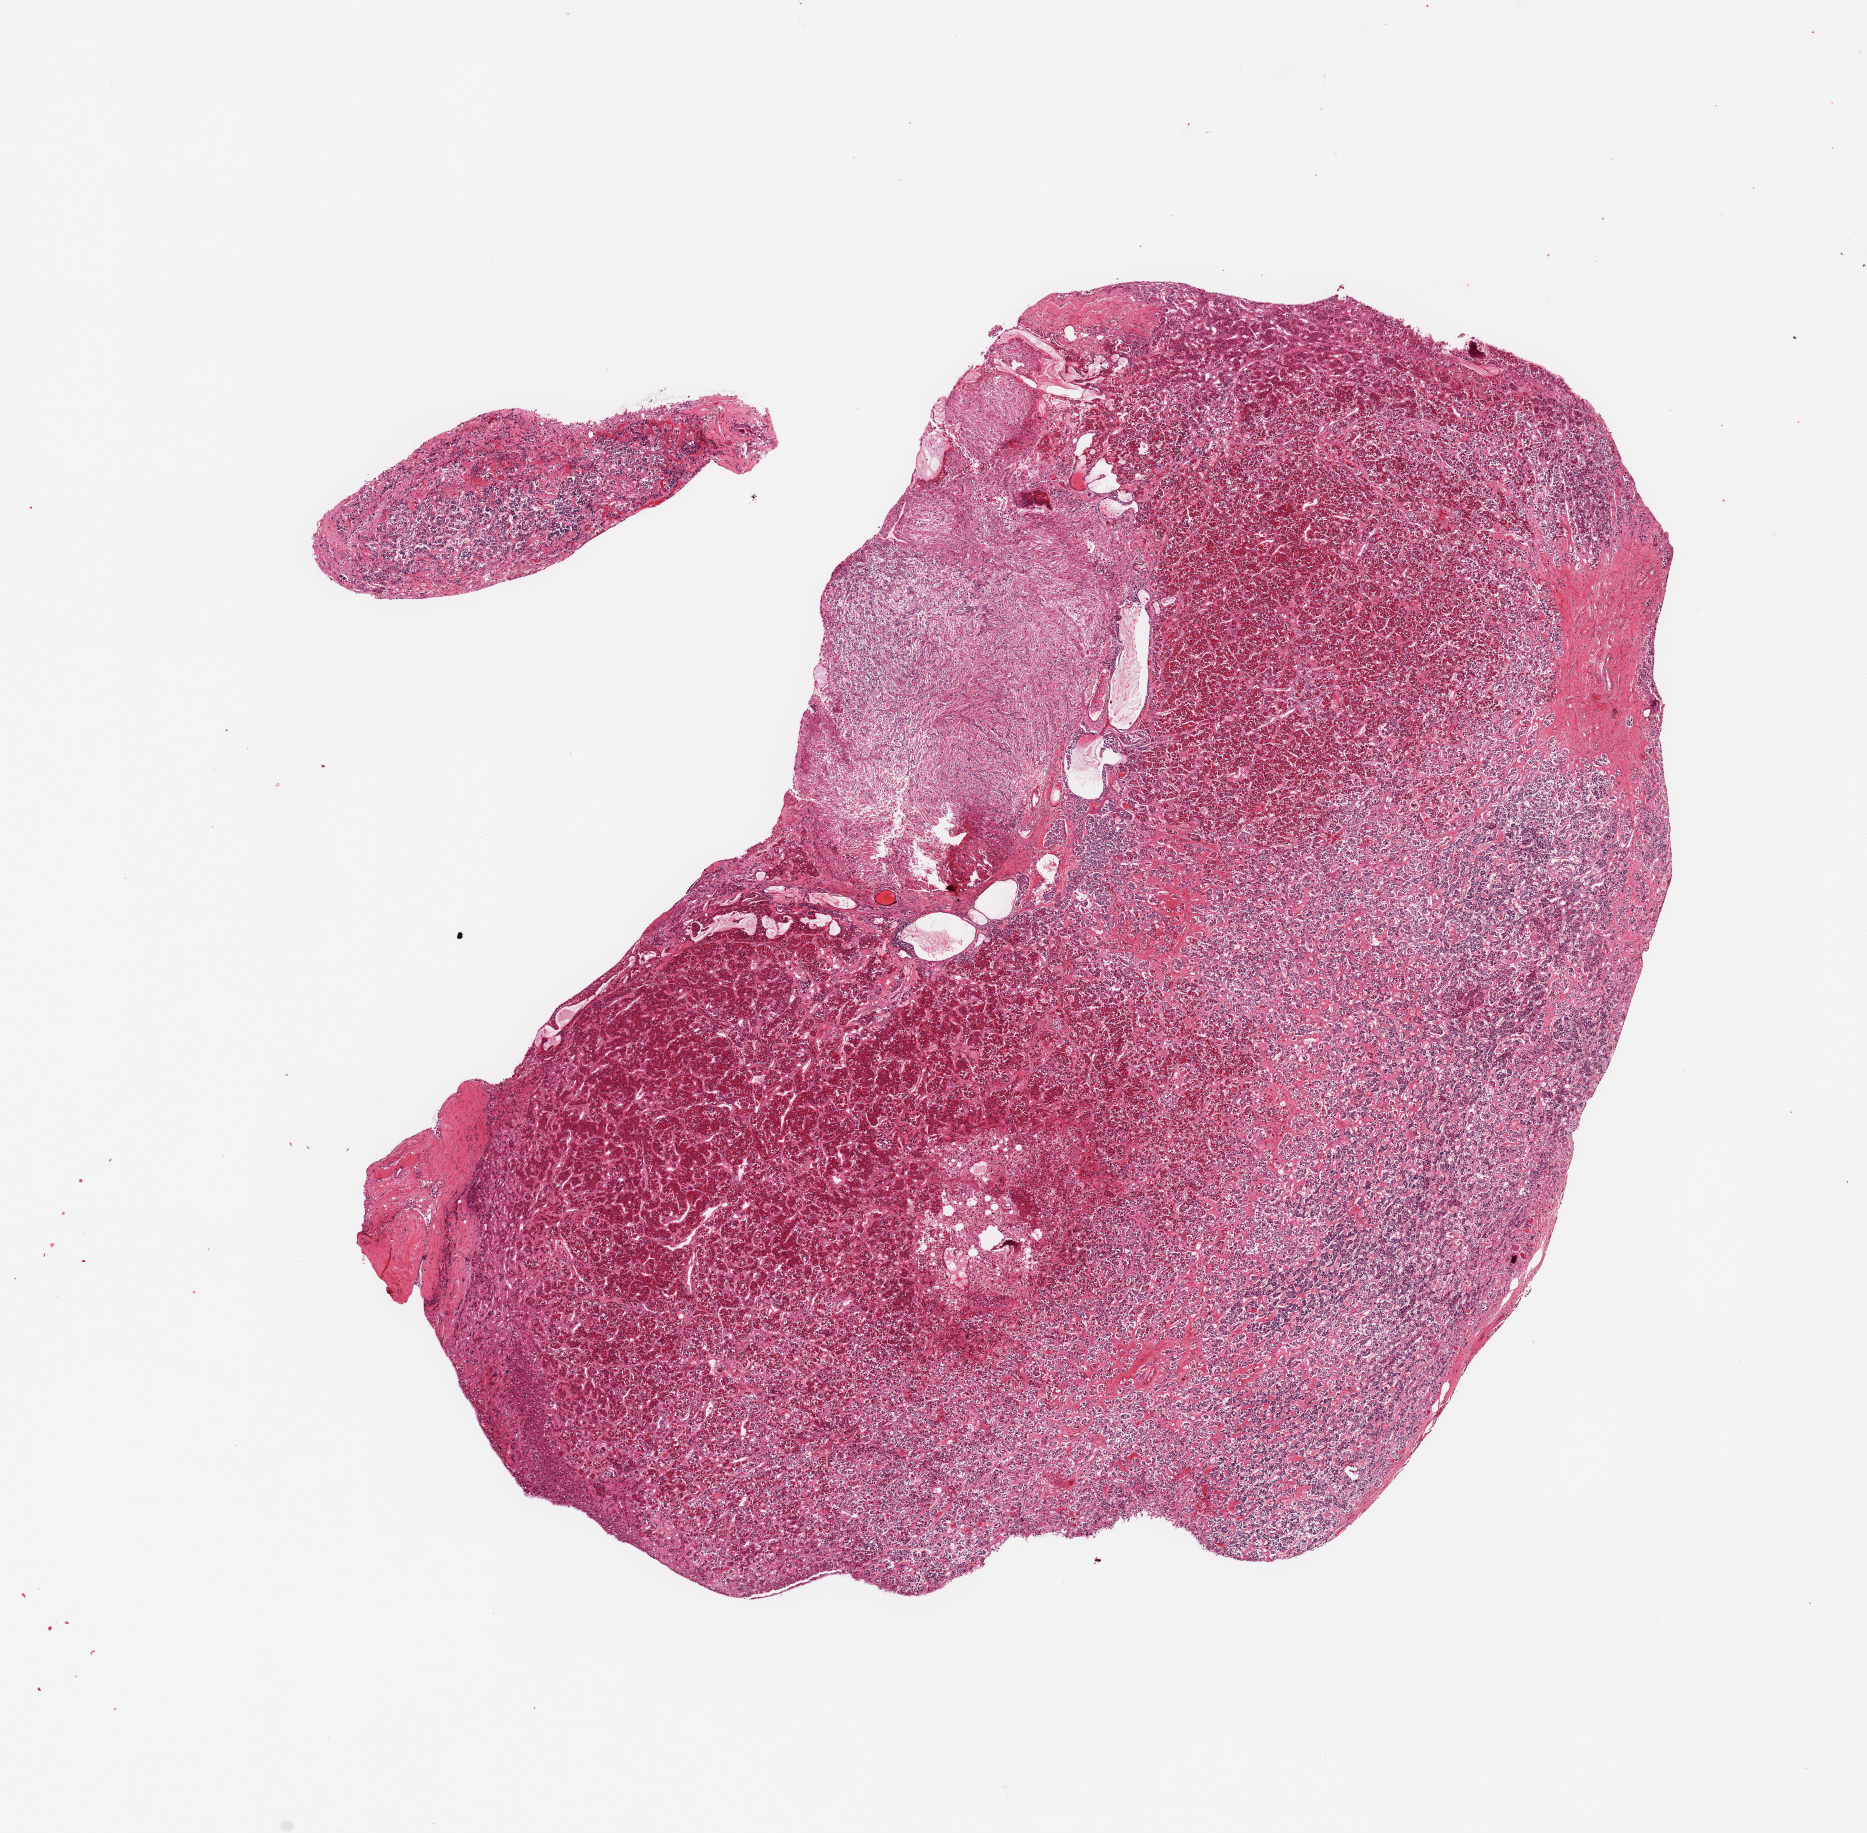
Hematoxylin and eosin (H&E) whole-slide image — low-resolution overview of the scanned area, about 14.8 x 14.5 mm (slide scanned at 20x); PAXgene-fixed paraffin-embedded (PFPE) section; sampled site (target tissue): pituitary; donor tissue sample. Male donor.
Reviewer comment on this tissue sample: 1 piece; adenohypophysis and neurohypophysis with Rathke cleft remnants/cyst.